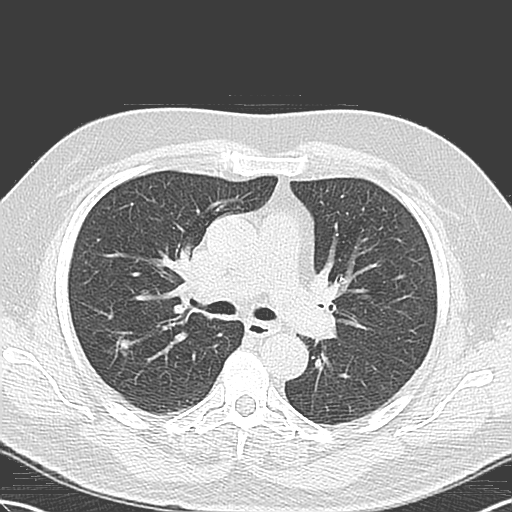
Low-dose screening chest CT, one axial slice; position 75 of 131 along the scan axis; lung window (W 1500 / L -600 HU); 3.2 mm slice thickness; 512 × 512 image matrix.
Structures marked on this image (outlined manually by an expert reader):
- lesion 1 (tumor, upper lobe of right lung): bounding box (x1, y1, x2, y2) in pixels: (120, 339, 133, 349)